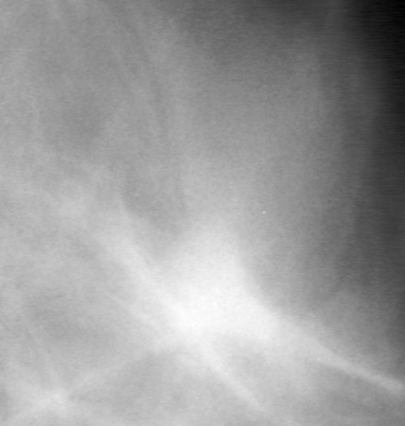
Cropped region of a digitized screen-film mammogram centred on a radiologist-marked abnormality, left breast, MLO view.
Finding: mass, shape oval, margins obscured; BI-RADS assessment category 0 (incomplete: needs additional imaging); subtlety rating 5 on a 1 (subtle) to 5 (obvious) scale; pathology (as recorded): benign.